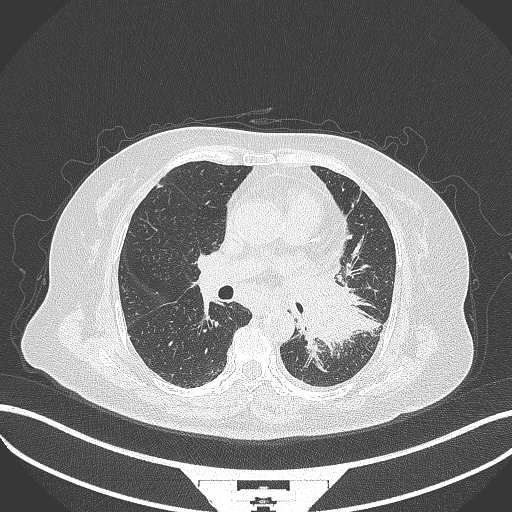
Chest CT, one axial slice. Slice 187 of 322 in the series (ordered by position). Reconstruction kernel B70f. Lung window (W 1500 / L -600 HU). 1 mm slice thickness. 512 × 512 image matrix, field of view 400 × 400 mm. Female patient, age 69 years. From the clinical record (not read from this slice): clinical TNM (as recorded): T2b N3 M1.
Outlined on this slice (bounding box drawn by a radiologist):
- lung tumour (recorded histology: adenocarcinoma): bounding box [x1, y1, x2, y2] px = [301, 280, 362, 346]